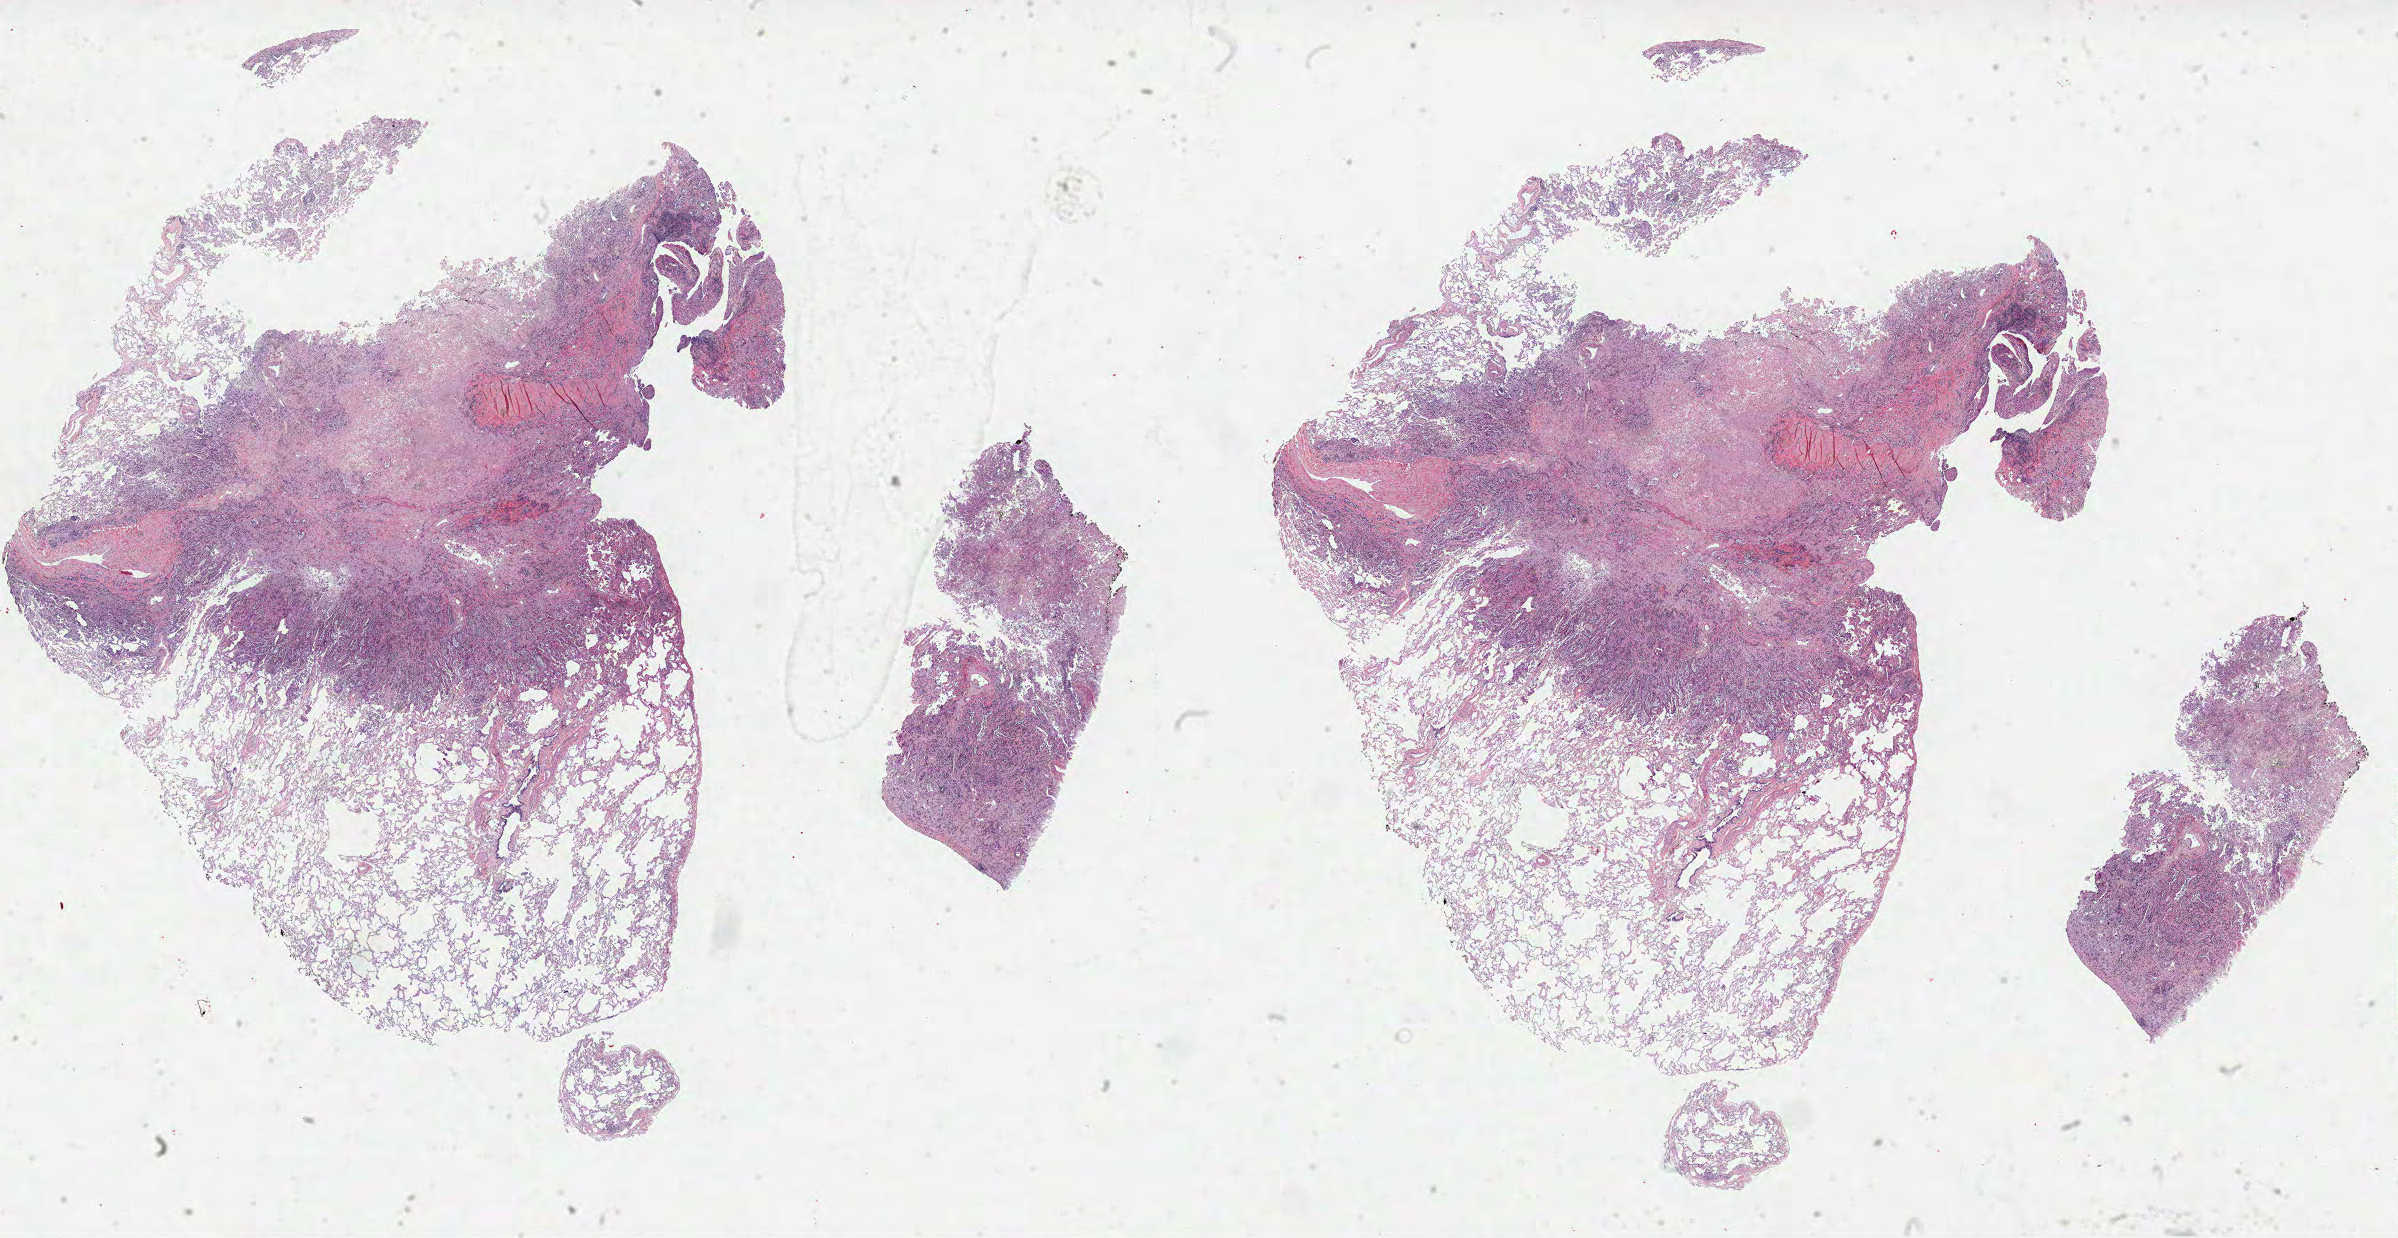
Whole-slide histology image, H&E — a low-resolution overview of the entire scanned area, about 38.7 x 20.0 mm; FFPE section; sample: primary tumour, lung. Female, age 49 years at initial diagnosis.
Laterality: right. AJCC pathologic stage: IV (7th edition). Histologic diagnosis: Adenocarcinoma, NOS (upper lobe, lung).